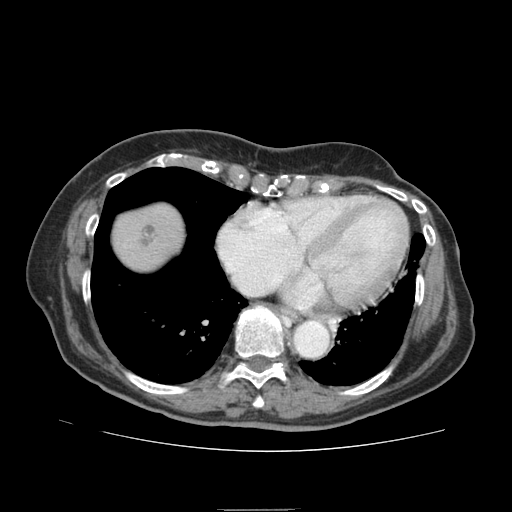
Contrast-enhanced abdominal CT (liver protocol), one axial slice; slice 80 of 95 in the series (ordered by position); reconstruction kernel STANDARD; 140 kVp; soft-tissue window (W 400 / L 40 HU); 2.5 mm slice thickness; 512 × 512 image matrix, field of view 360 × 360 mm. From the clinical record (not read from this slice): diagnosis: hepatocellular carcinoma (patient treated with transarterial chemoembolisation; whether this scan precedes or follows treatment is not stated here); TNM stage (as recorded): Stage-IVA; Child-Pugh class: B; tumour nodularity: uninodular.
Annotated regions visible in this slice (semi-automatically segmented with operator editing):
- abdominal aorta: box from (x=295, y=321) to (x=327, y=356) px
- liver parenchyma outside the tumour (the mass and vessels are separate outlines, so this box may not span the whole liver): (x=112, y=204)–(x=184, y=270)